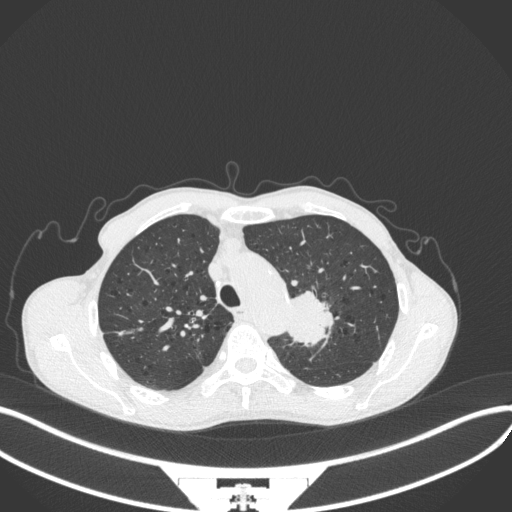
Chest CT, one axial slice; position 319 of 394 along the scan axis; lung window (W 1500 / L -600 HU); 1 mm slice thickness; 512 × 512 image matrix, field of view 400 × 400 mm. Patient: male, 65 years. Case-level facts recorded for this patient, not image findings: clinical TNM (as recorded): T2b N0 M0; histopathological grade: G2.
Annotated regions visible in this slice (bounding box drawn by a radiologist):
- lung tumour (recorded histology: adenocarcinoma): bounding box <283,285,333,353> (left, top, right, bottom; pixels)